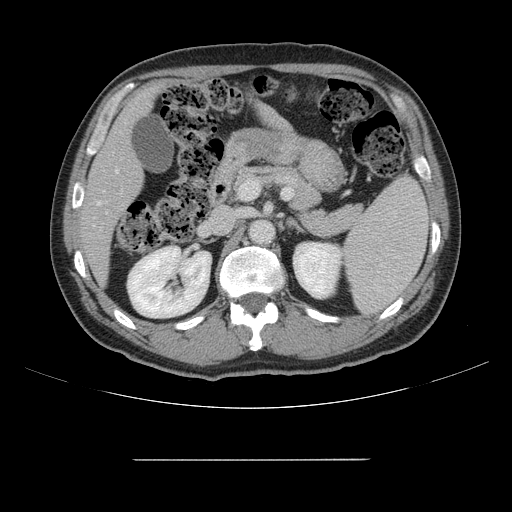
Contrast-enhanced abdominal CT, one axial slice. Position 77 of 164 along the scan axis. 120 kVp. Intravenous contrast given. Soft-tissue window (W 400 / L 40 HU). 2.5 mm slice thickness. 512 × 512 image matrix, field of view 404 × 404 mm. Male patient, age 54 years. Case-level facts recorded for this patient, not image findings: diagnosis: colorectal cancer liver metastases, imaged before liver resection; multiple liver metastases: yes; largest metastasis: 1 cm; disease in both lobes: no.
Outlined on this slice (manually delineated by an expert):
- hepatic veins: box from (x=98, y=169) to (x=119, y=205) px
- liver: (x=85, y=90)–(x=284, y=280)
- planned liver remnant (the part of the liver to remain after resection): (x=85, y=90)–(x=154, y=280)